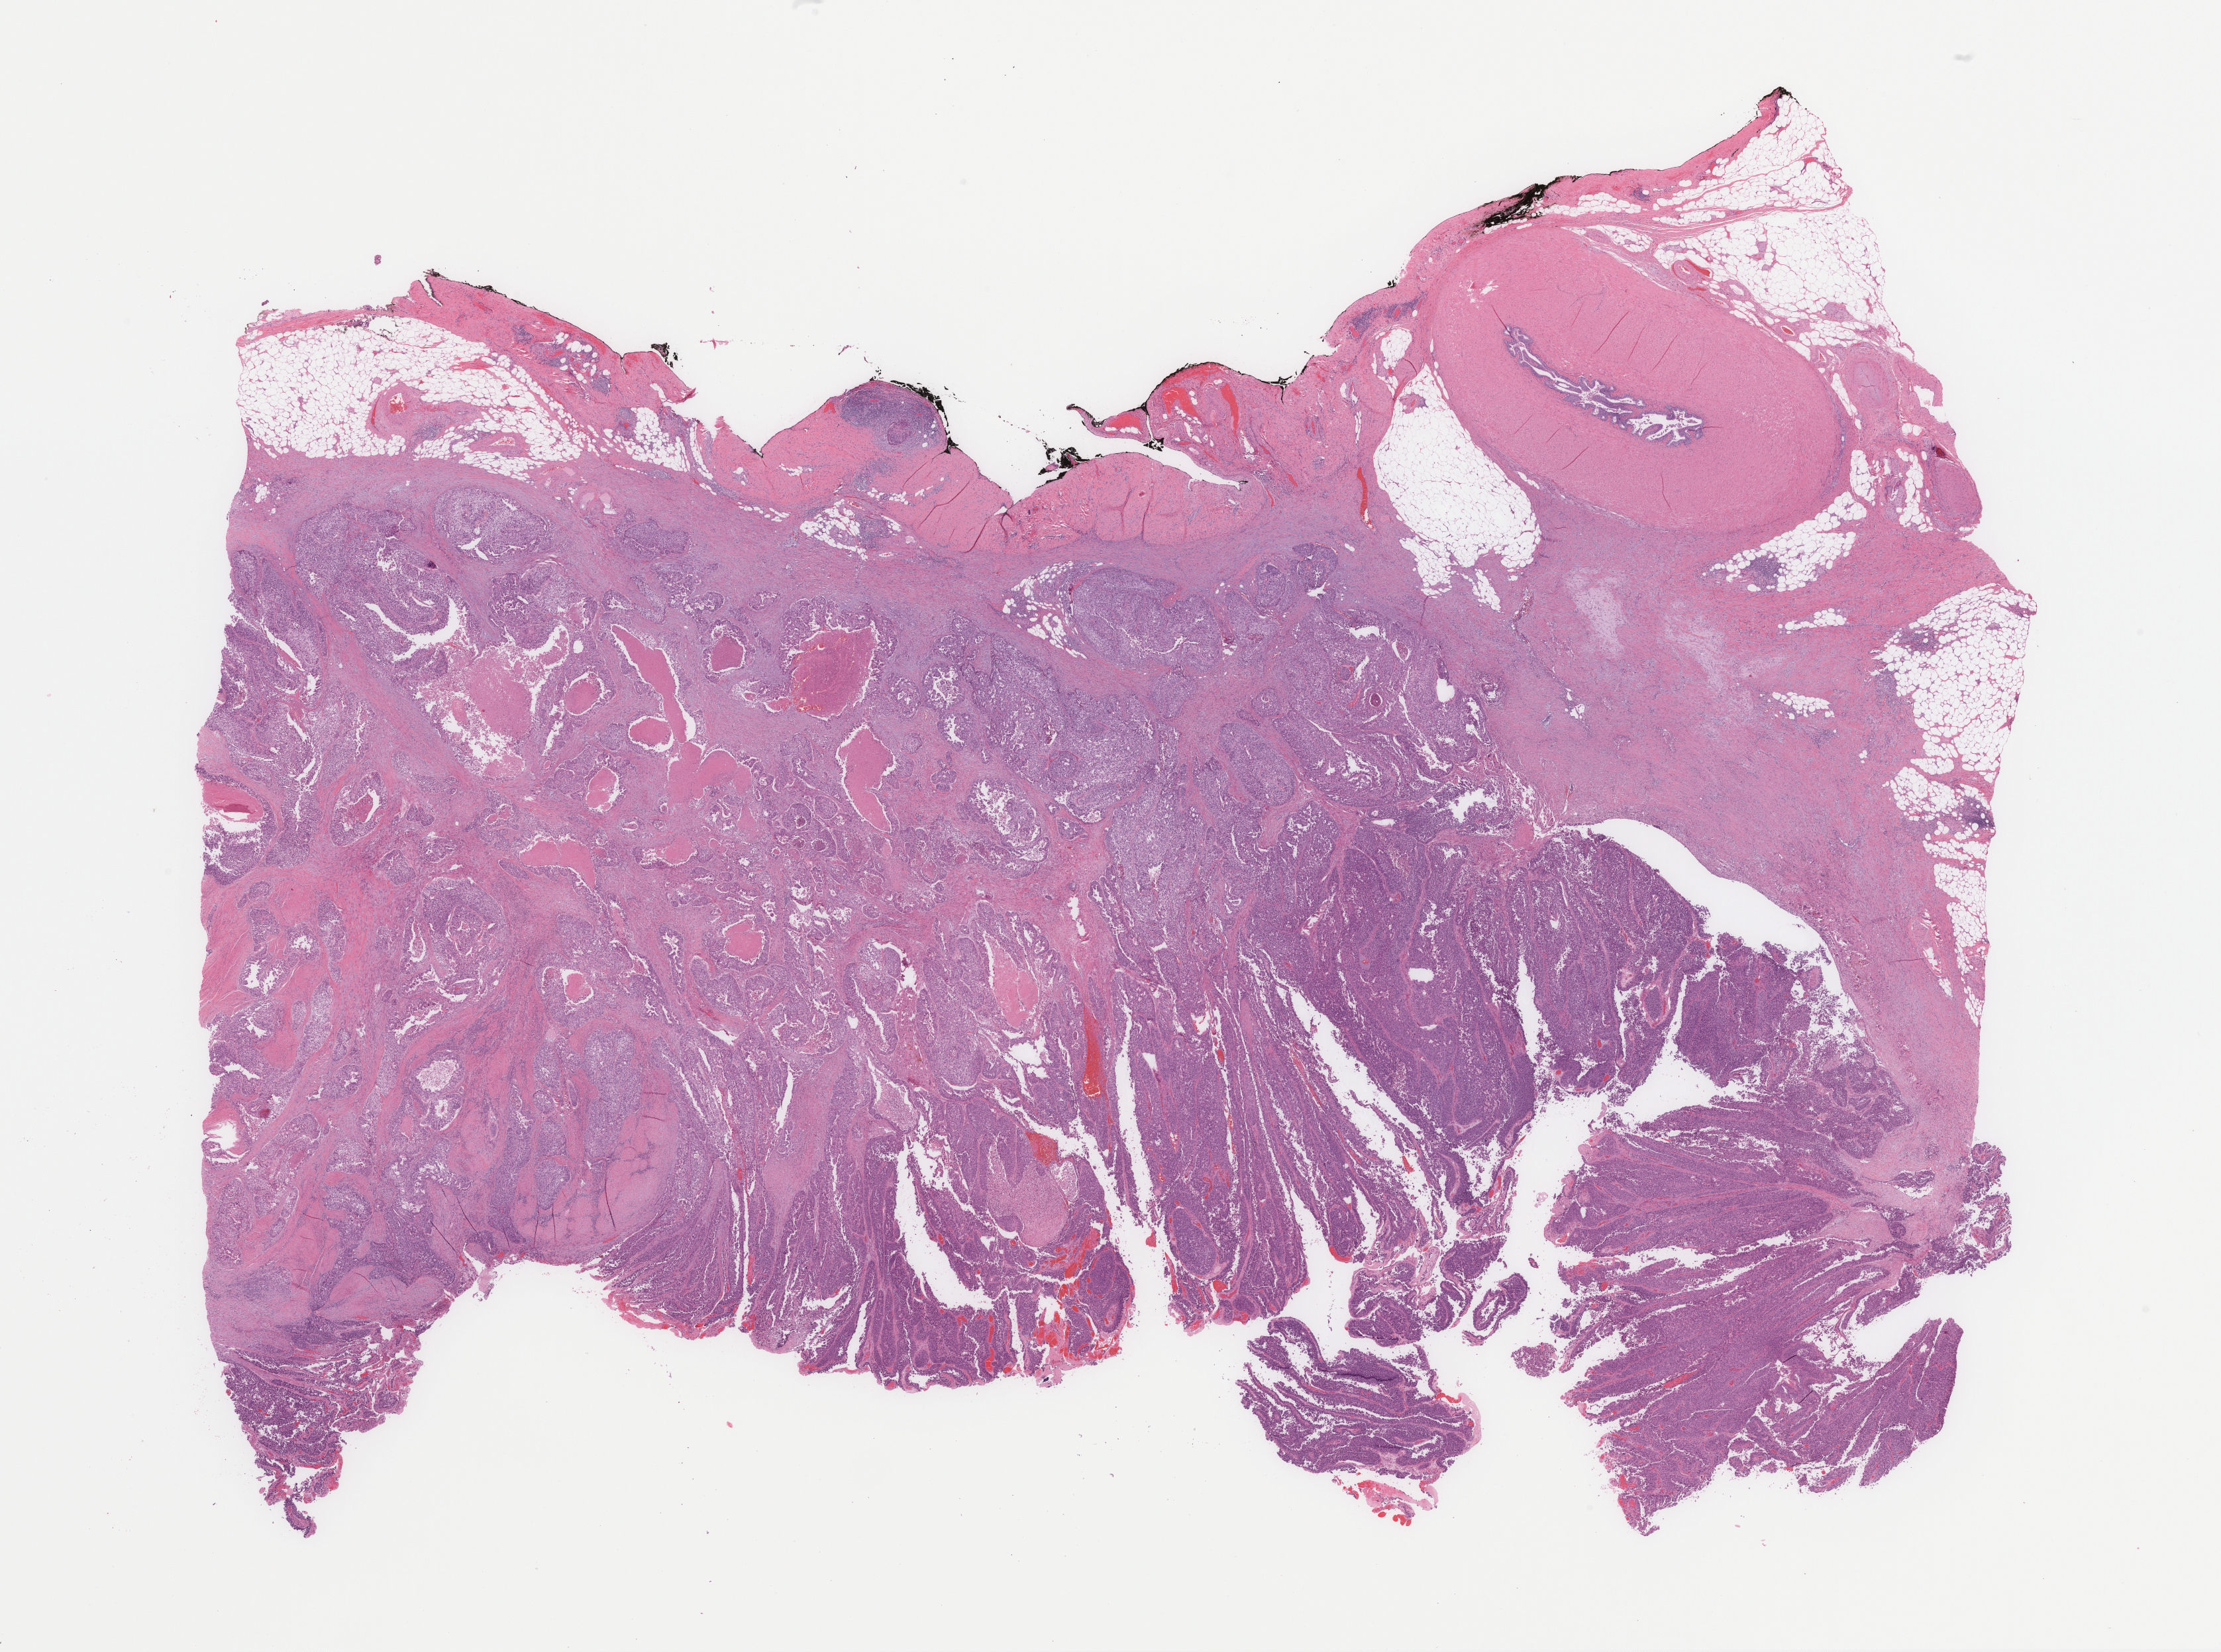
Digitized H&E-stained tissue section (whole slide), shown as a low-resolution overview of the whole scanned area (about 26.6 x 19.8 mm, slide scanned at 40x), formalin-fixed paraffin-embedded (FFPE) diagnostic section, sample: primary tumour, bladder. Male, age 47 years at initial diagnosis.
Pathologic diagnosis: Transitional cell carcinoma (posterior wall of bladder).